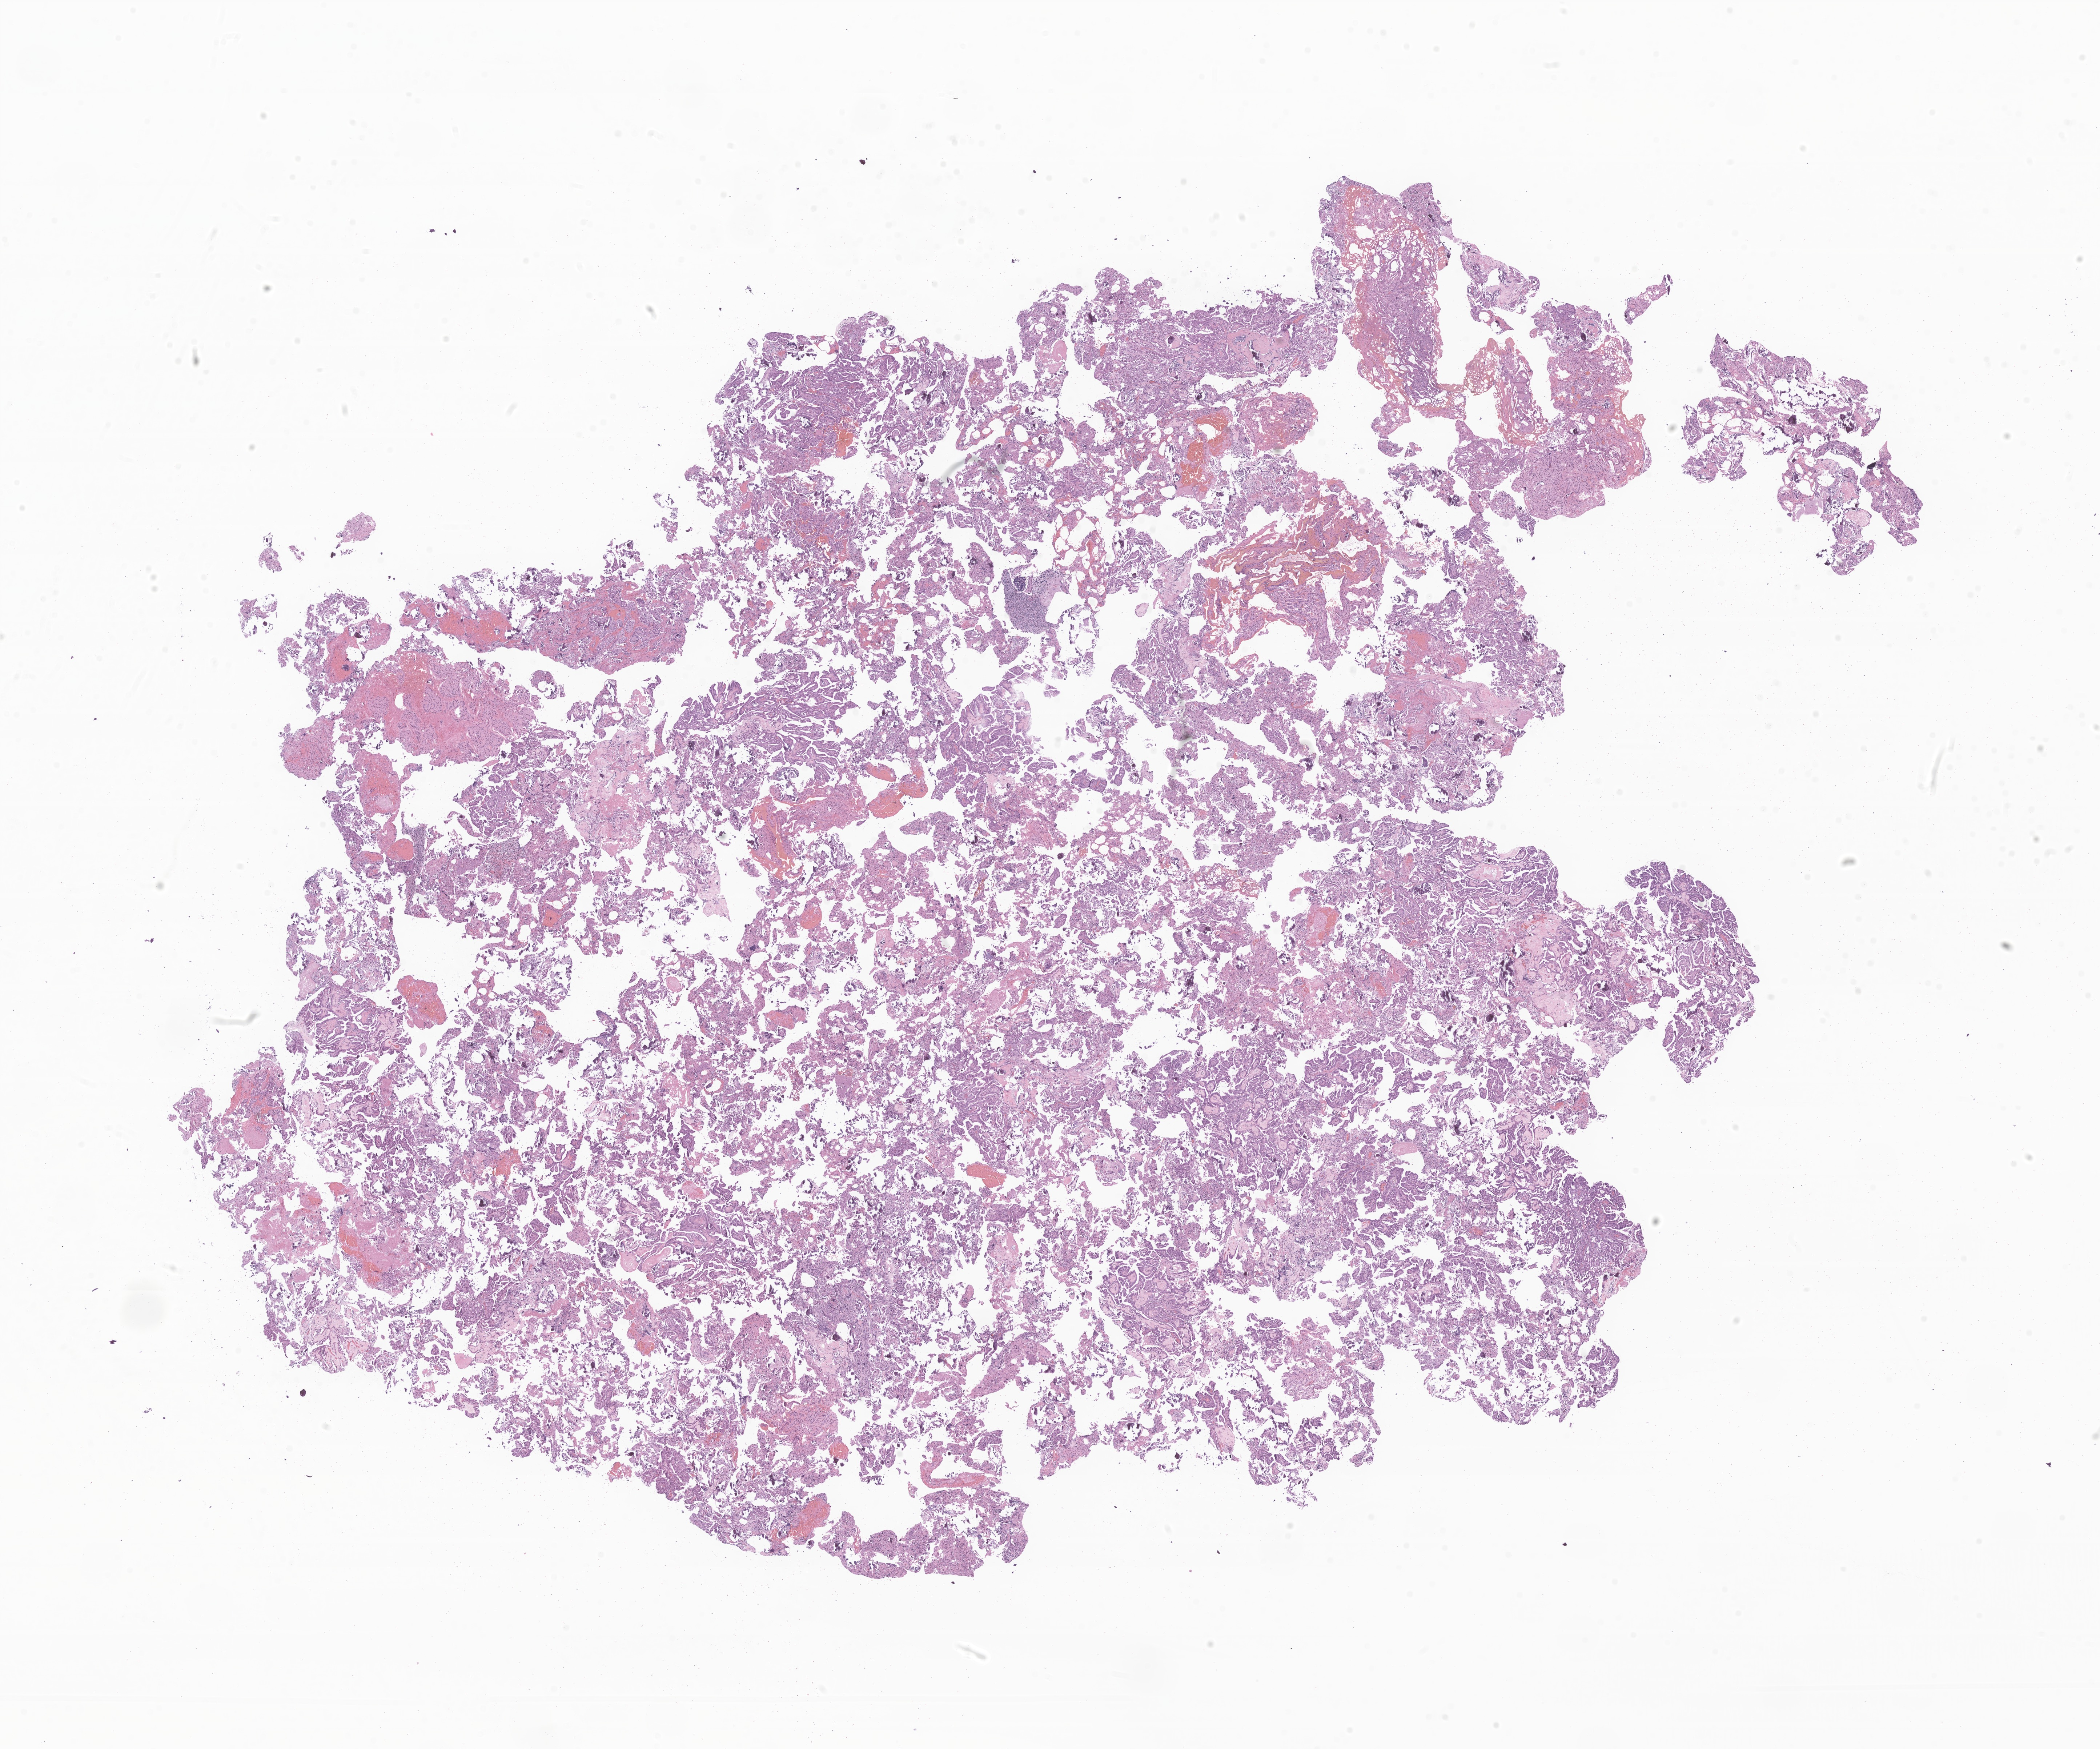
Hematoxylin and eosin (H&E) whole-slide image of tumor tissue from the brain, a low-resolution overview of the entire scanned area, about 24.4 x 20.3 mm. Formalin-fixed paraffin-embedded section. Patient male; age 187 months (15 years 7 months).
Diagnosis: Neoplasm, uncertain whether benign or malignant.